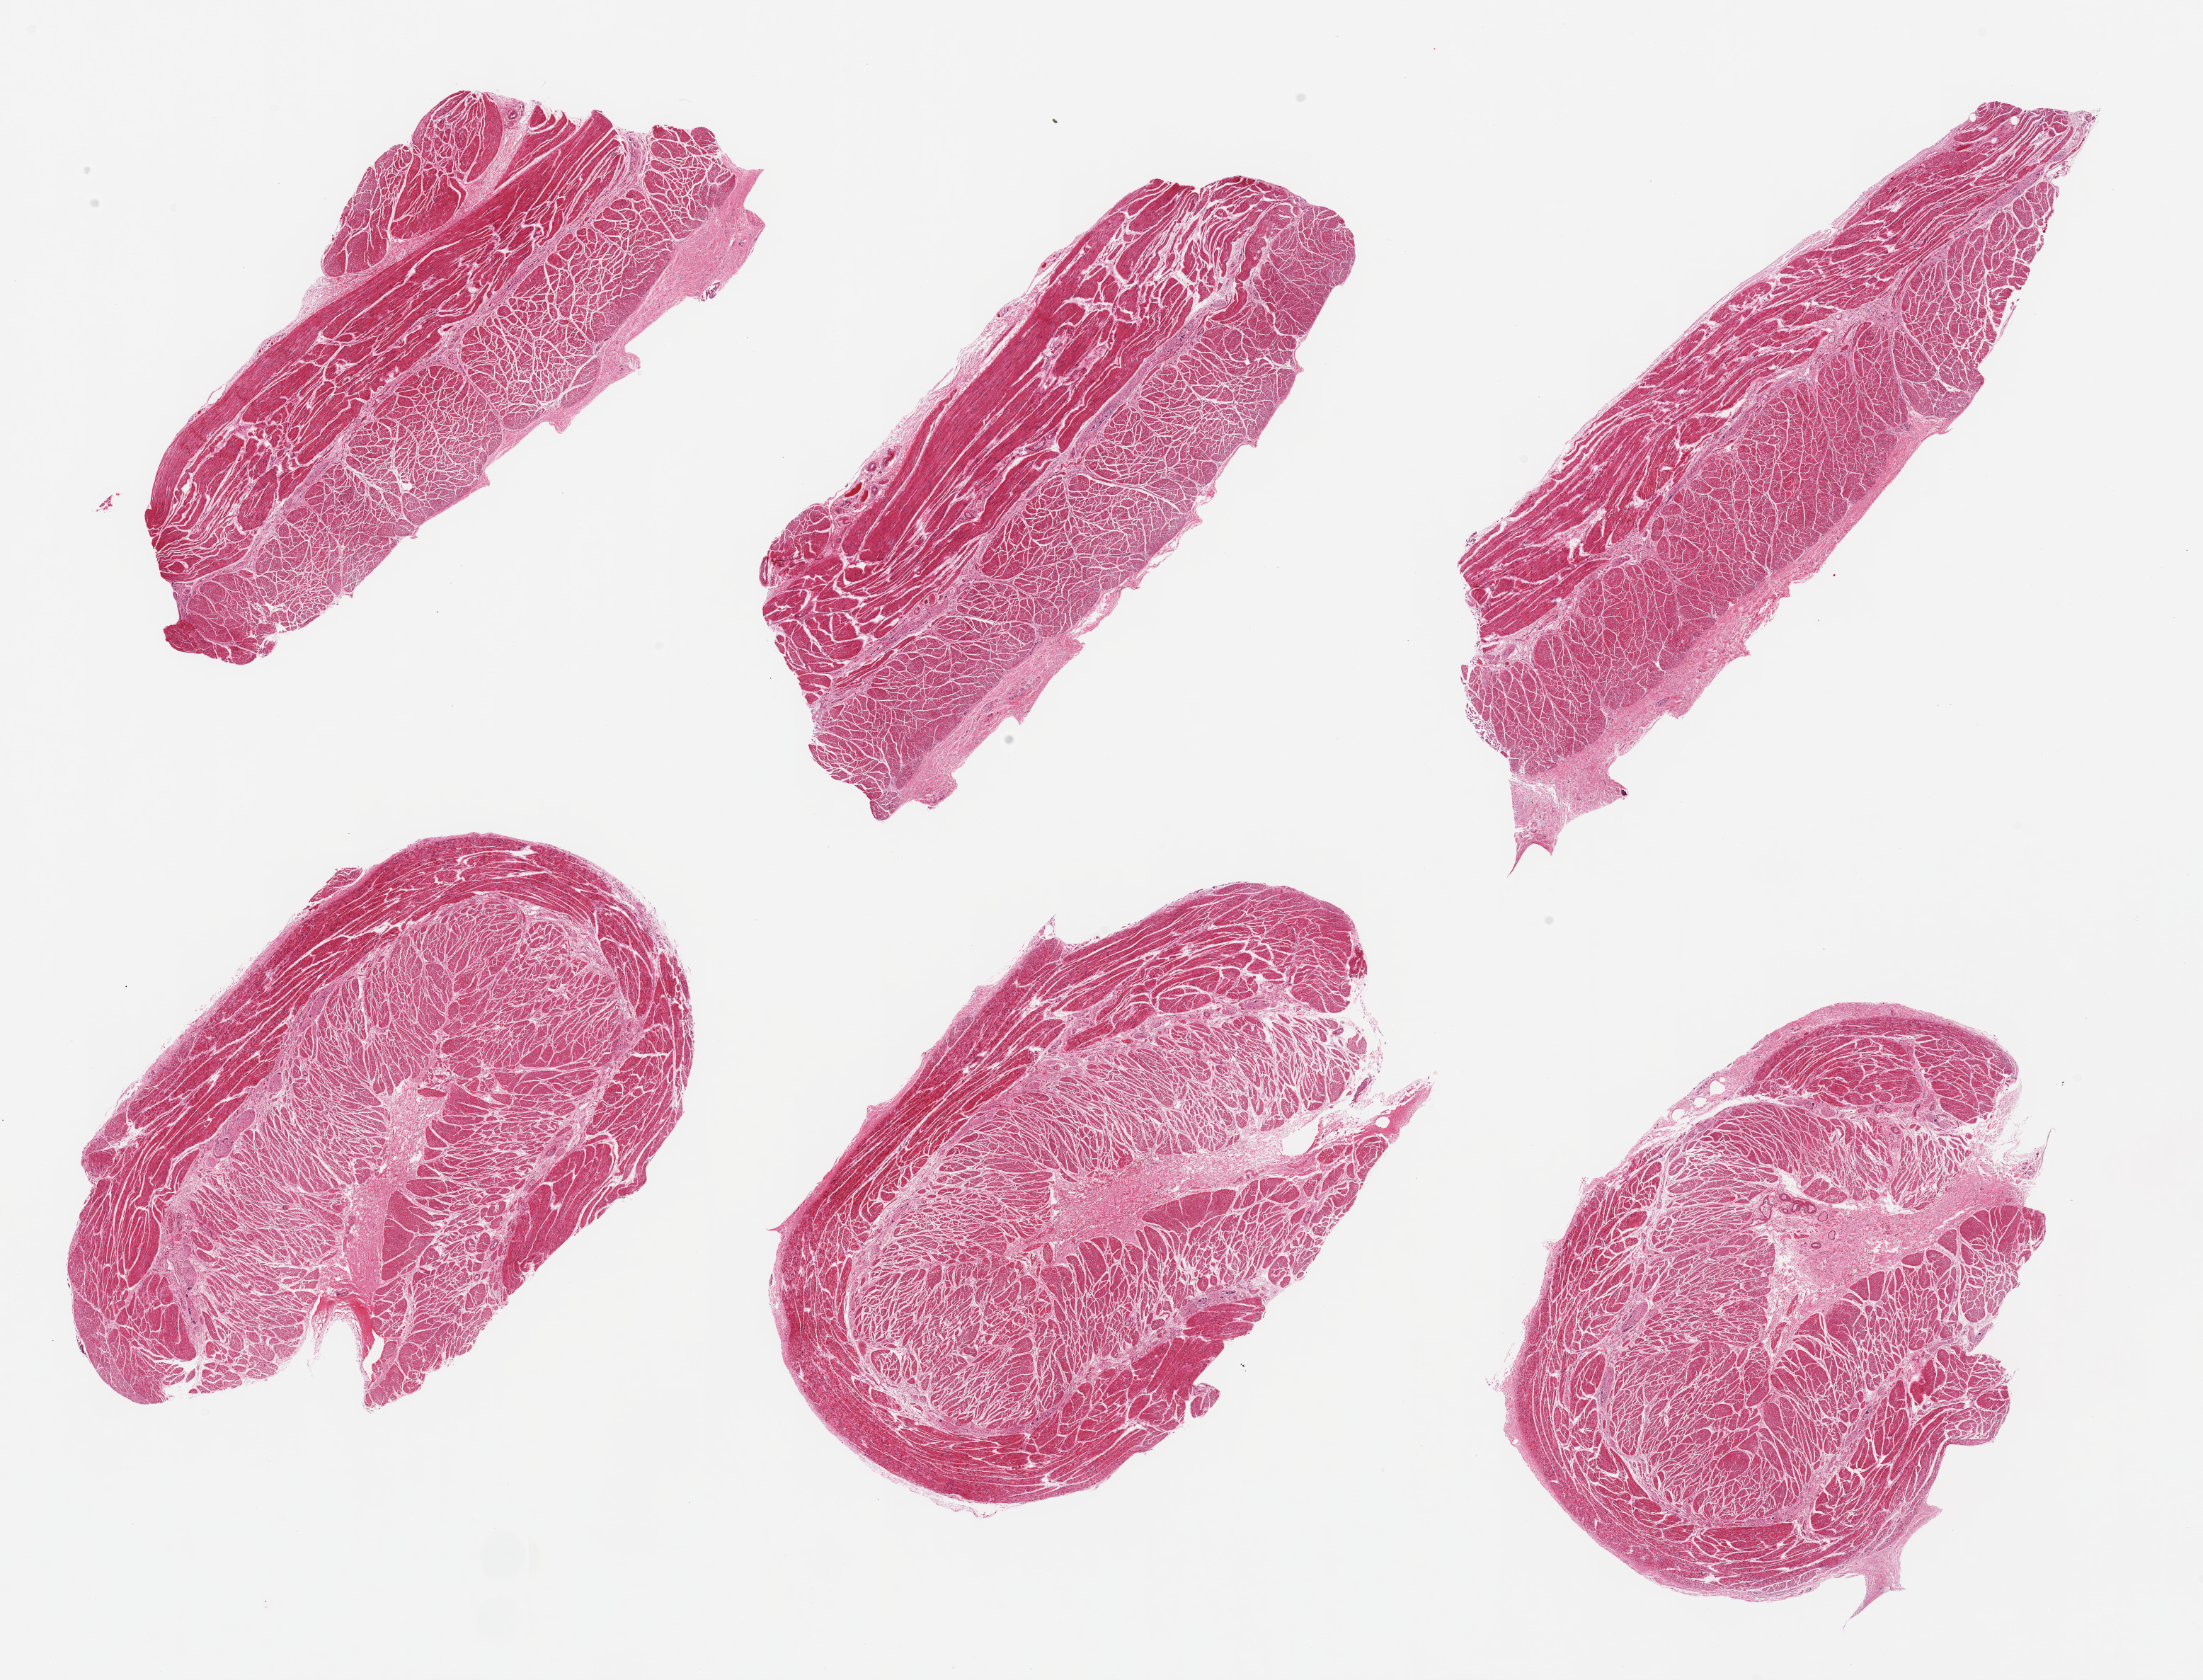
Hematoxylin and eosin (H&E) whole-slide image, brightfield — a low-resolution overview of the entire scanned area, about 24.6 x 18.8 mm (acquisition: 20x scan), PAXgene-fixed, paraffin-embedded tissue, sampled site (target tissue): esophageal muscle, tissue donor sample. Donor sex: female.
Pathologist's review note for this sample: 6 pieces; well dissected.